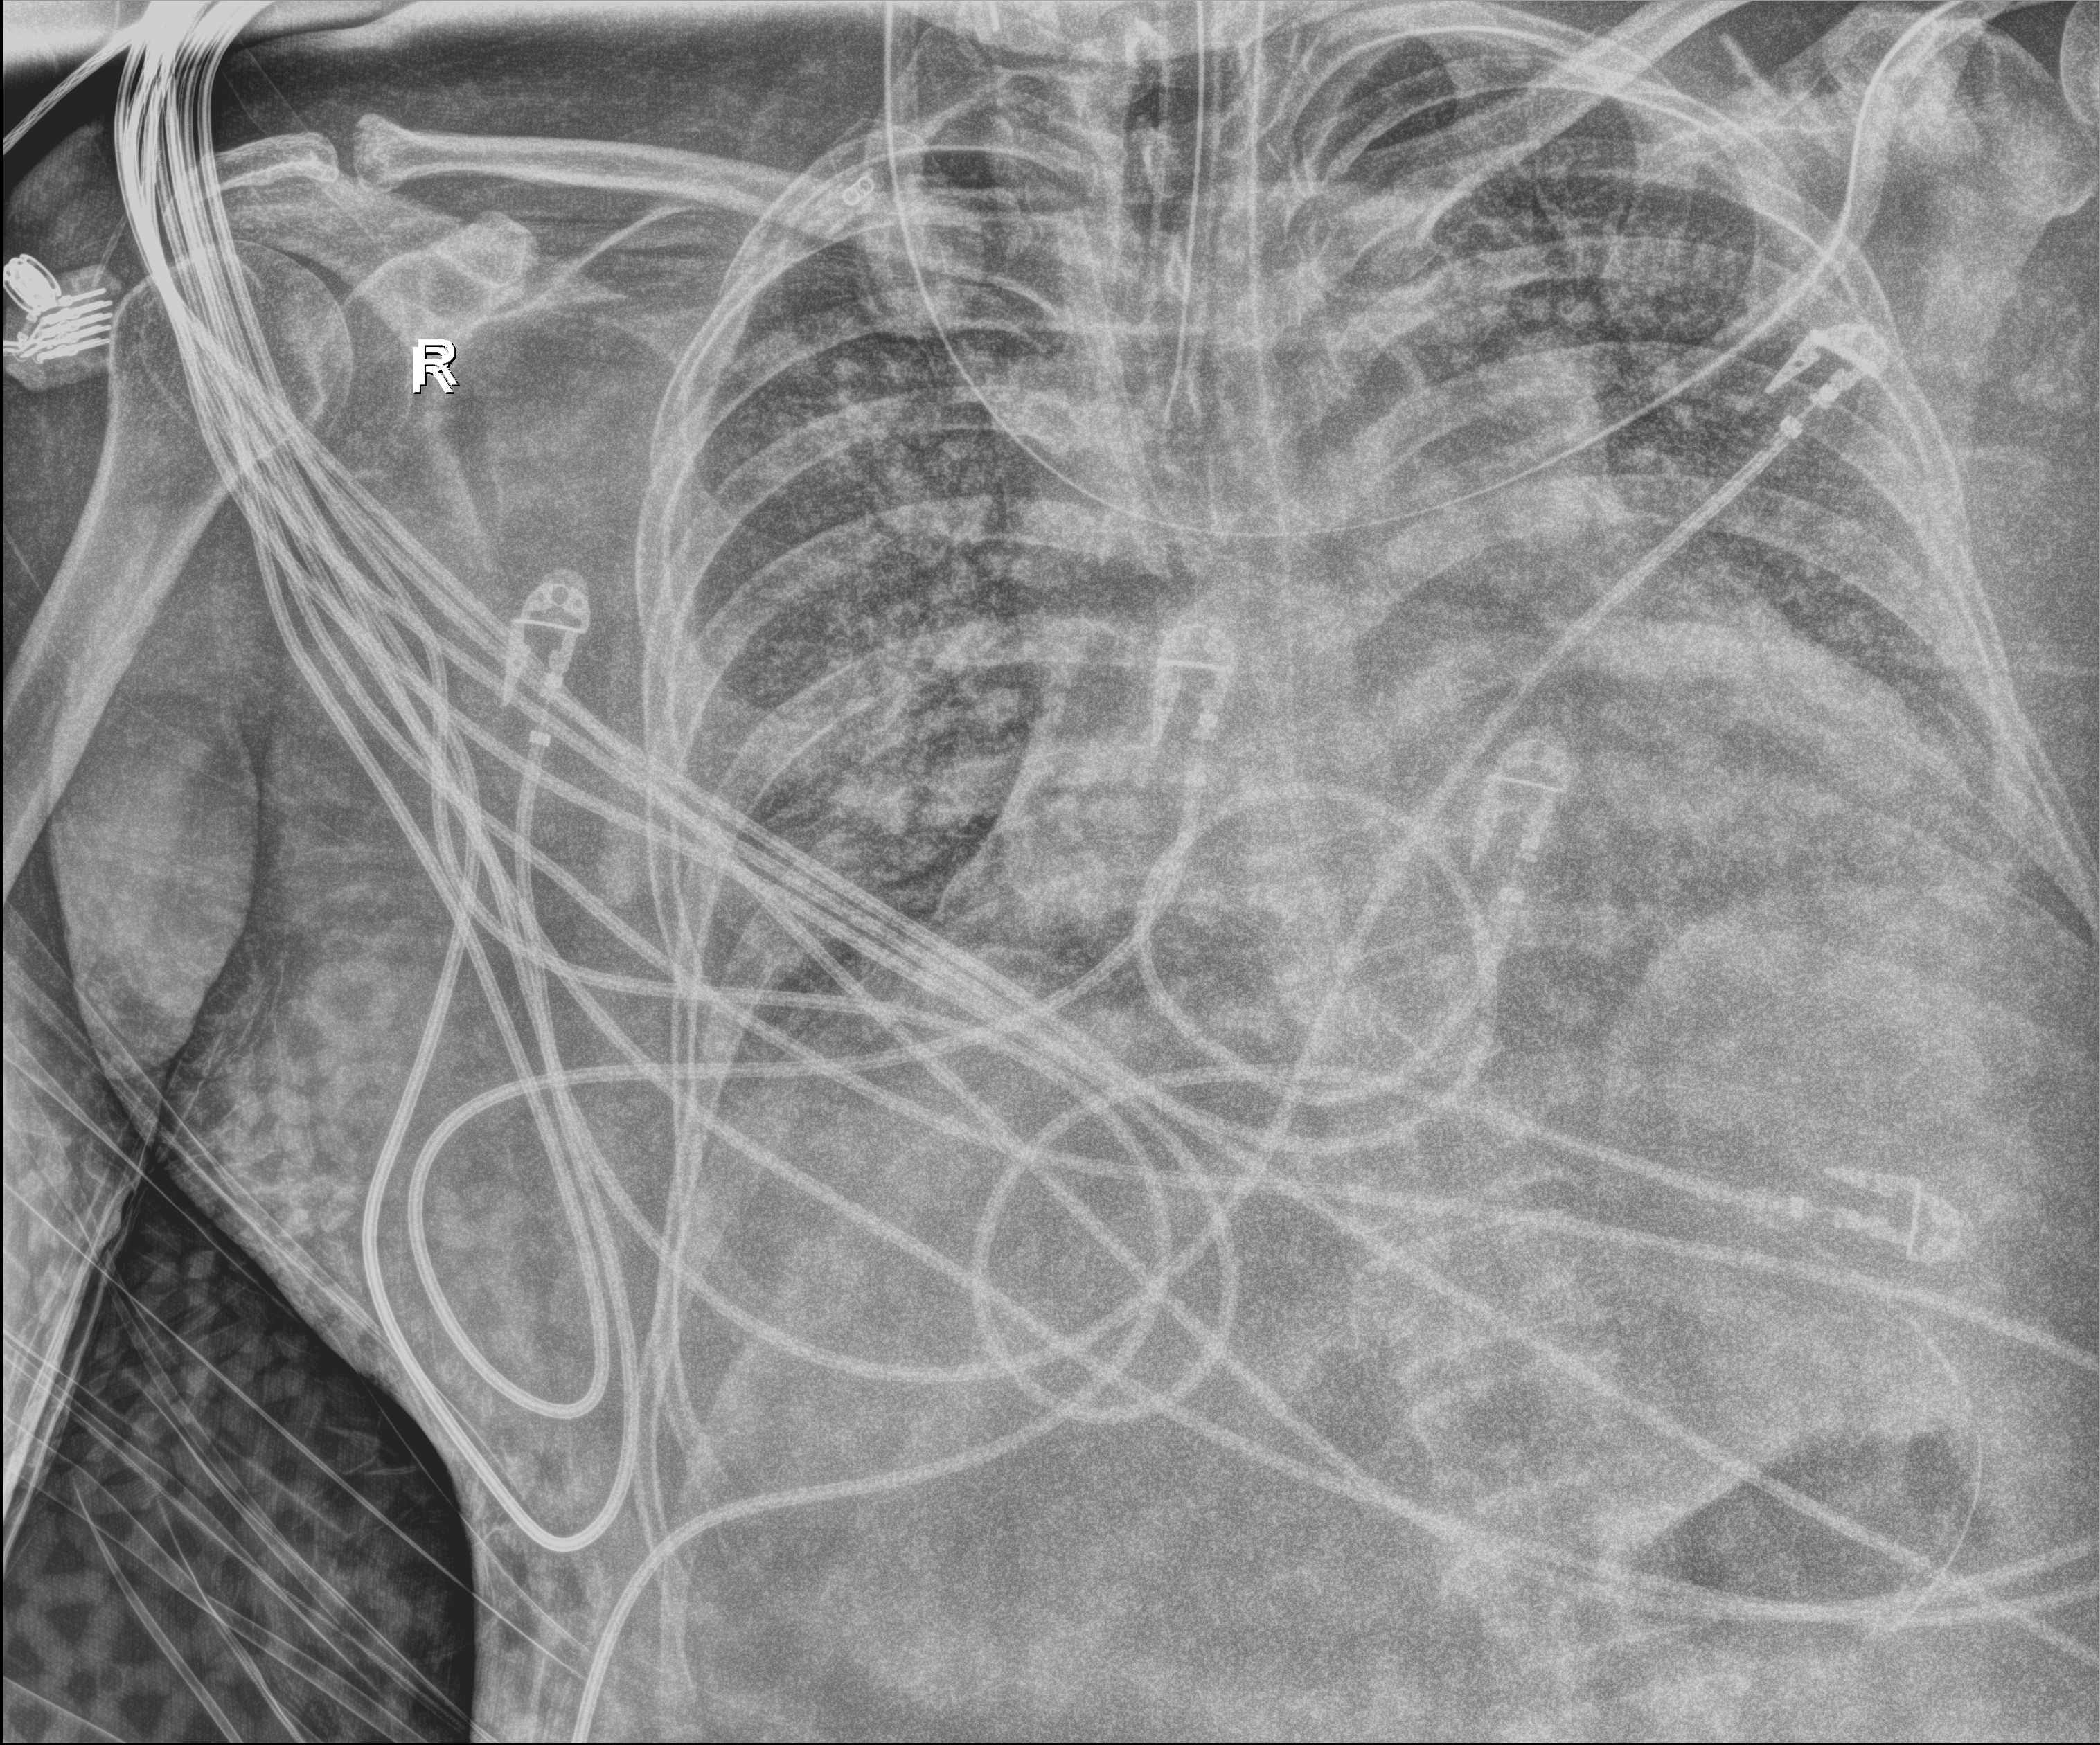
Bedside chest radiograph (digital radiography). Adult patient hospitalised with COVID-19, age 18–59 years.
Admission-level facts for this patient (not findings on this image; timing relative to this image not recorded): length of hospital stay: 48 days.